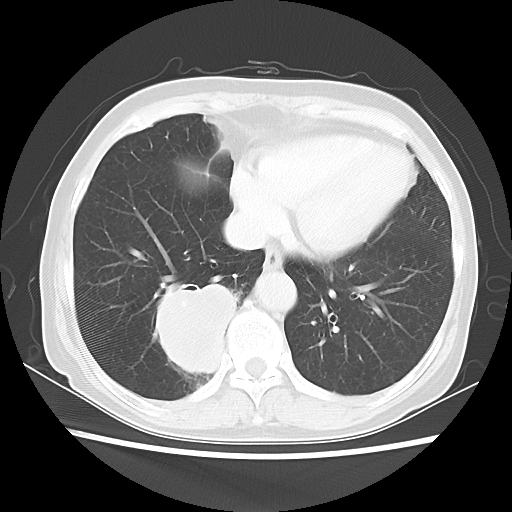
Chest CT, one axial slice; position 17 of 56 along the scan axis; lung window (W 1500 / L -600 HU); 5 mm slice thickness; 512 × 512 image matrix, field of view 332 × 332 mm. Patient: female, 66 years. From the clinical record (not read from this slice): clinical TNM (as recorded): T2 N3 M0.
Annotated regions visible in this slice (rectangle marked by the reading radiologist):
- lung tumour (recorded histology: small cell carcinoma): bounding box (x1, y1, x2, y2) in pixels: (154, 274, 248, 392)